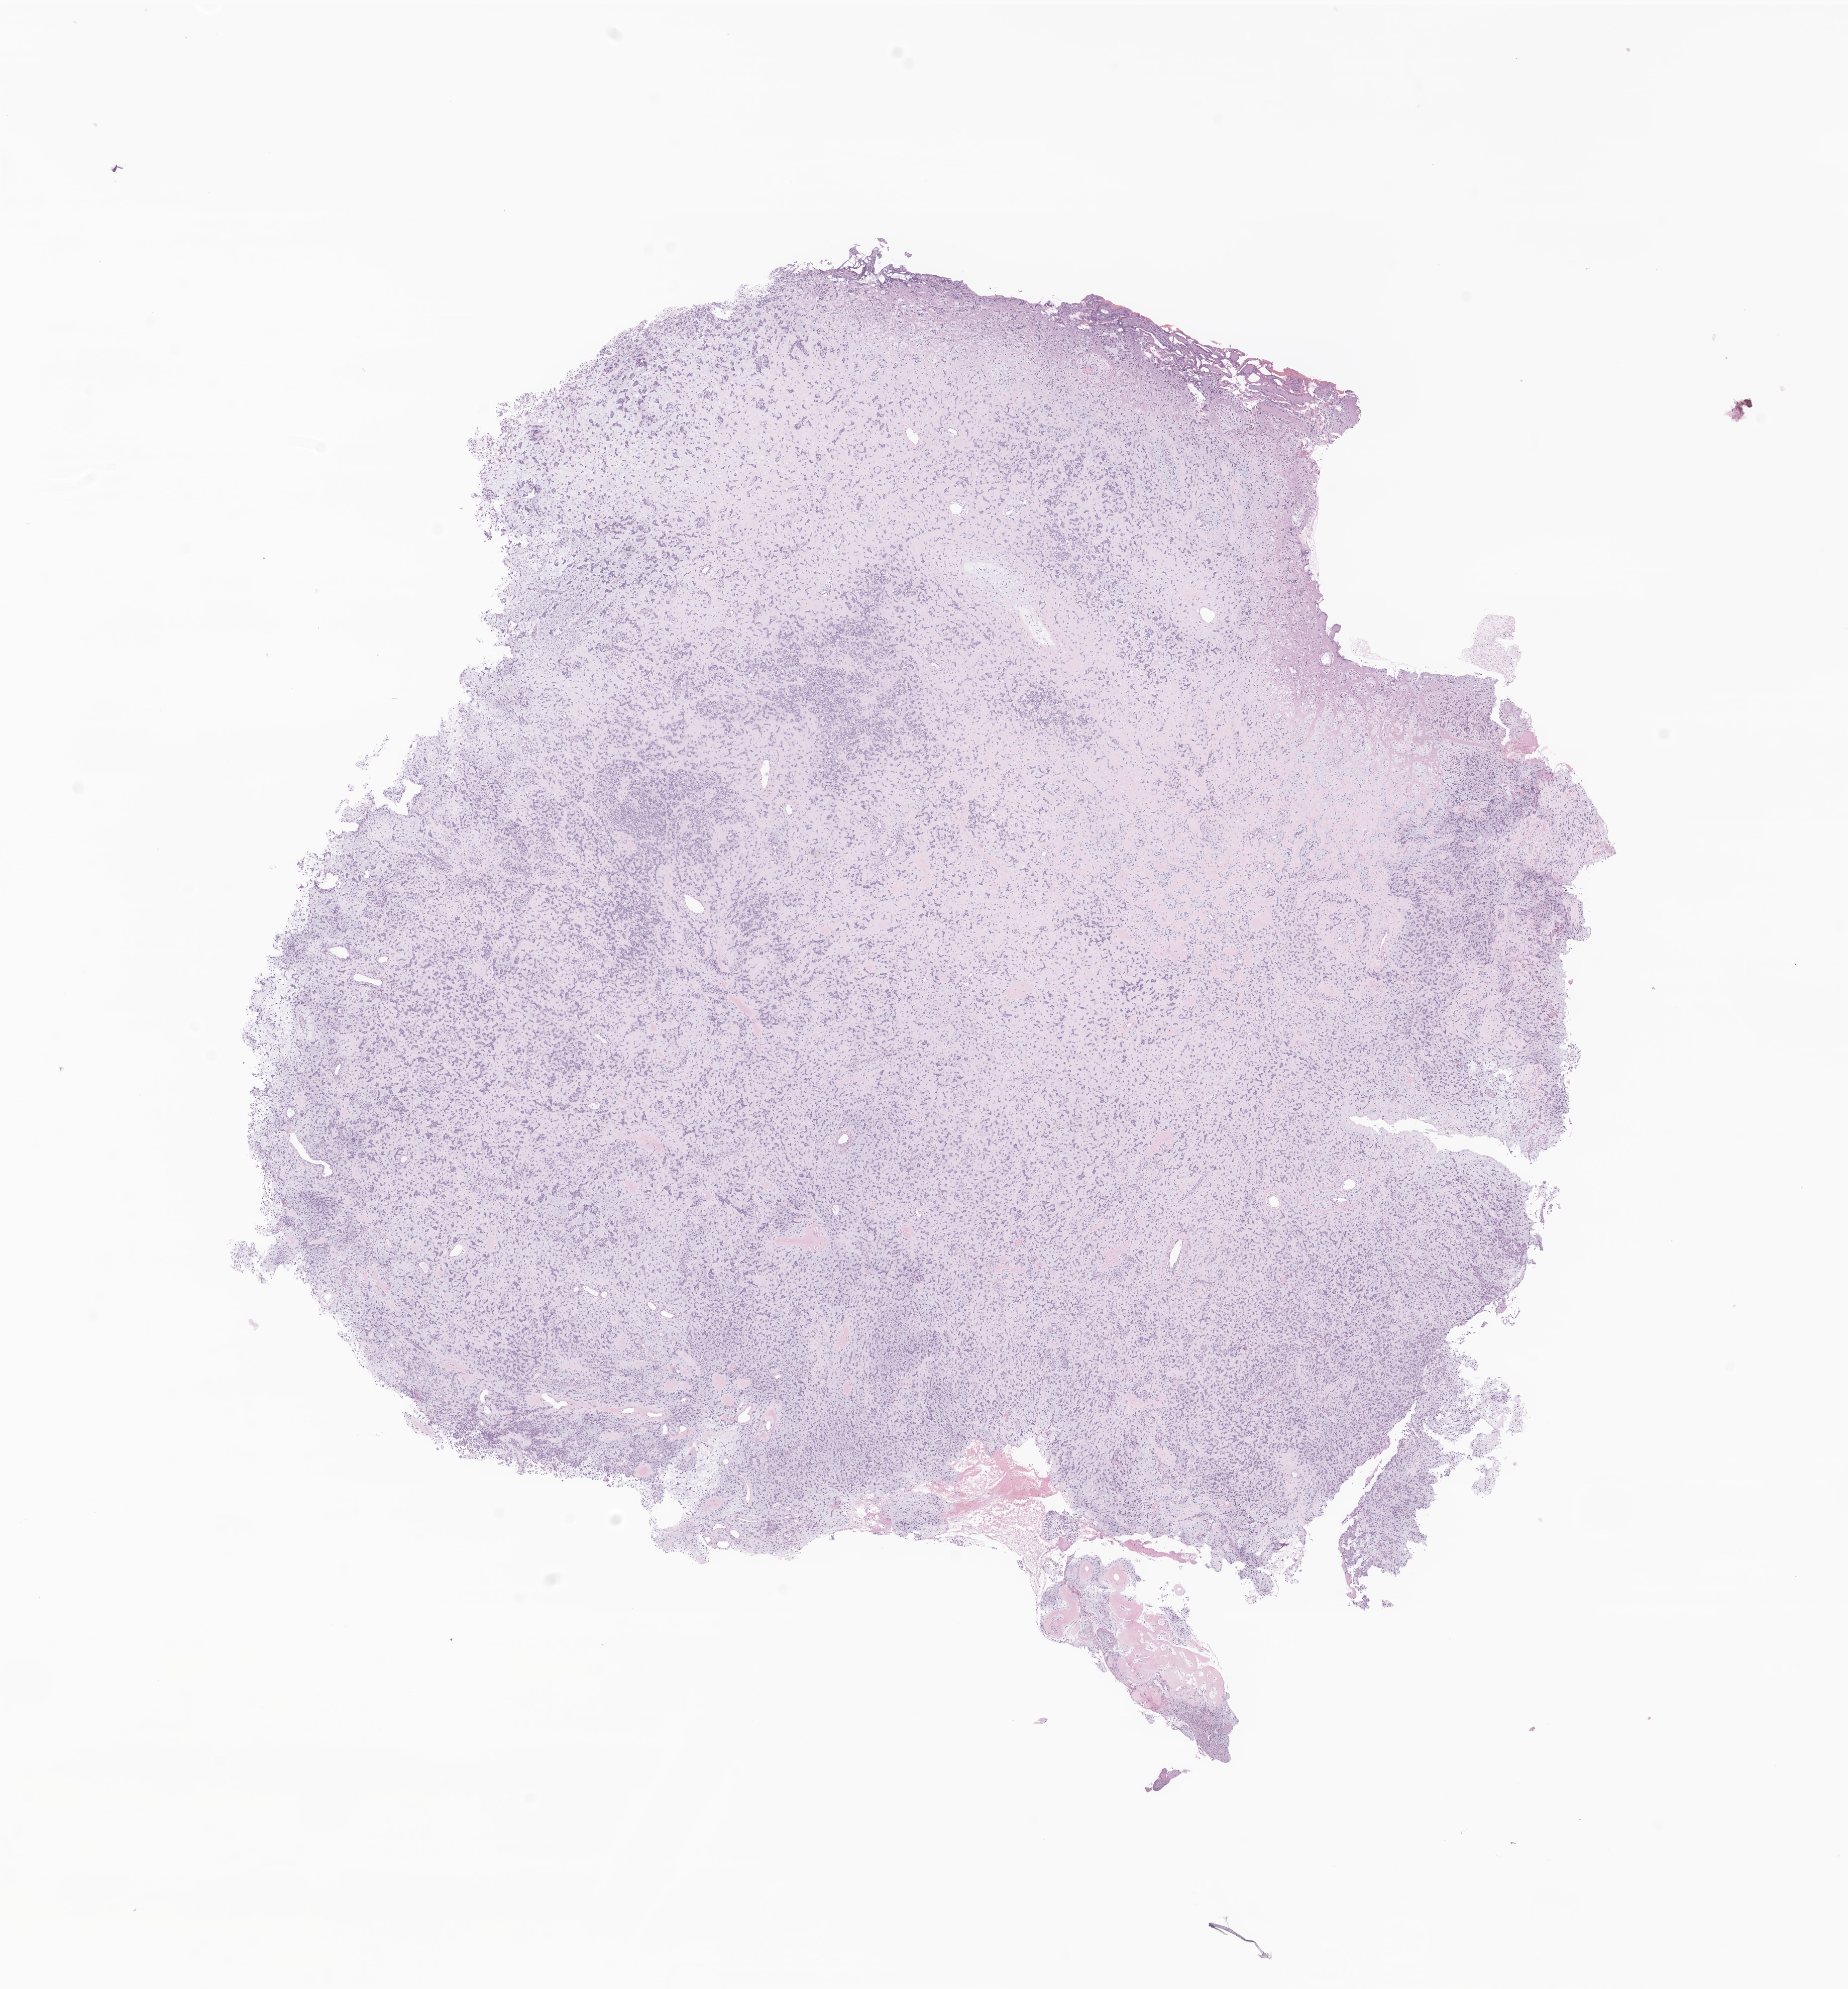
Hematoxylin and eosin (H&E) whole-slide image of tumor tissue from the brain — whole scanned area (about 15.5 x 16.7 mm) shown as a low-resolution overview, FFPE section. Female patient, age 241 months (20 years 1 month).
• diagnosis (ICD-O-3 morphology term): Neoplasm, malignant